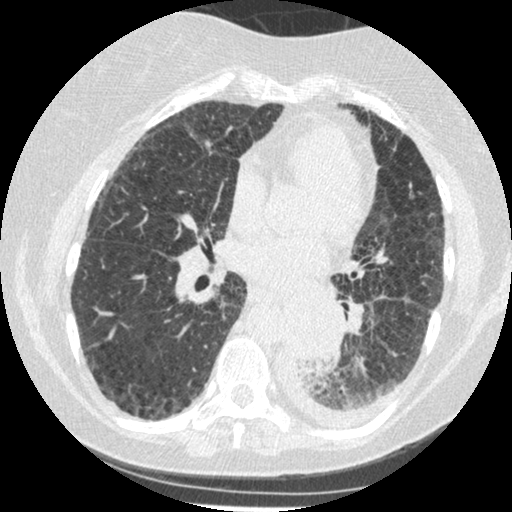
Low-dose screening chest CT, axial slice. Third annual screen. Lung window (W 1500 / L -600 HU). Standard (soft-tissue) reconstruction kernel (STANDARD). 120 kVp. Slice 231 of 341 in the series. 512 × 512 image matrix. Female, age 60 years at enrolment. Former smoker at enrolment.
• Expert reader's lesion annotation, bounding box (x1, y1, x2, y2) in pixels: (275, 304, 343, 375).
• Screening reader's record for this exam (one nodule recorded; not confirmed to be the boxed lesion): non-calcified nodule or mass ≥4 mm, left lower lobe, 54 × 38 mm, smooth margins, soft tissue attenuation, pre-existing on the prior screen: yes; interval growth: yes.
• Participant outcome: lung cancer diagnosed 15 days after this screen — small cell carcinoma, NOS, left lower lobe, undifferentiated (G4), stage IV (AJCC 6th edition), 69 mm at pathology.